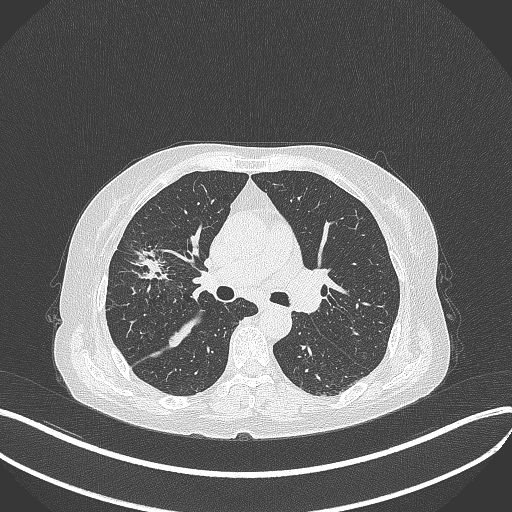
Chest CT, one axial slice. Position 239 of 429 along the scan axis. Lung window (W 1500 / L -600 HU). 512 × 512 image matrix, field of view 400 × 400 mm. Female patient, age 69 years. Case-level facts recorded for this patient, not image findings: clinical TNM (as recorded): T1b N3 M0.
Annotated regions visible in this slice (rectangle marked by the reading radiologist):
- lung tumour (recorded histology: small cell carcinoma): bounding box [x1, y1, x2, y2] px = [121, 243, 176, 289]